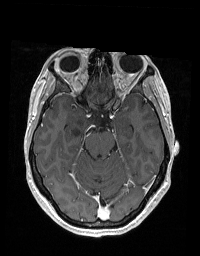
Brain MRI from a brain-tumour surgery series, one axial slice; slice 120 of 192 in the series (ordered by position); T1-weighted post-contrast; 1 mm slice thickness; 200 × 256 image matrix. Case-level facts recorded for this patient, not image findings: histopathology: Glioblastoma; WHO grade: 2; IDH mutation: no; tumour location: Right Skull Base Temporal.
Outlined on this slice (expert manual segmentation):
- tumour: bounding box <72,113,102,136> (left, top, right, bottom; pixels)